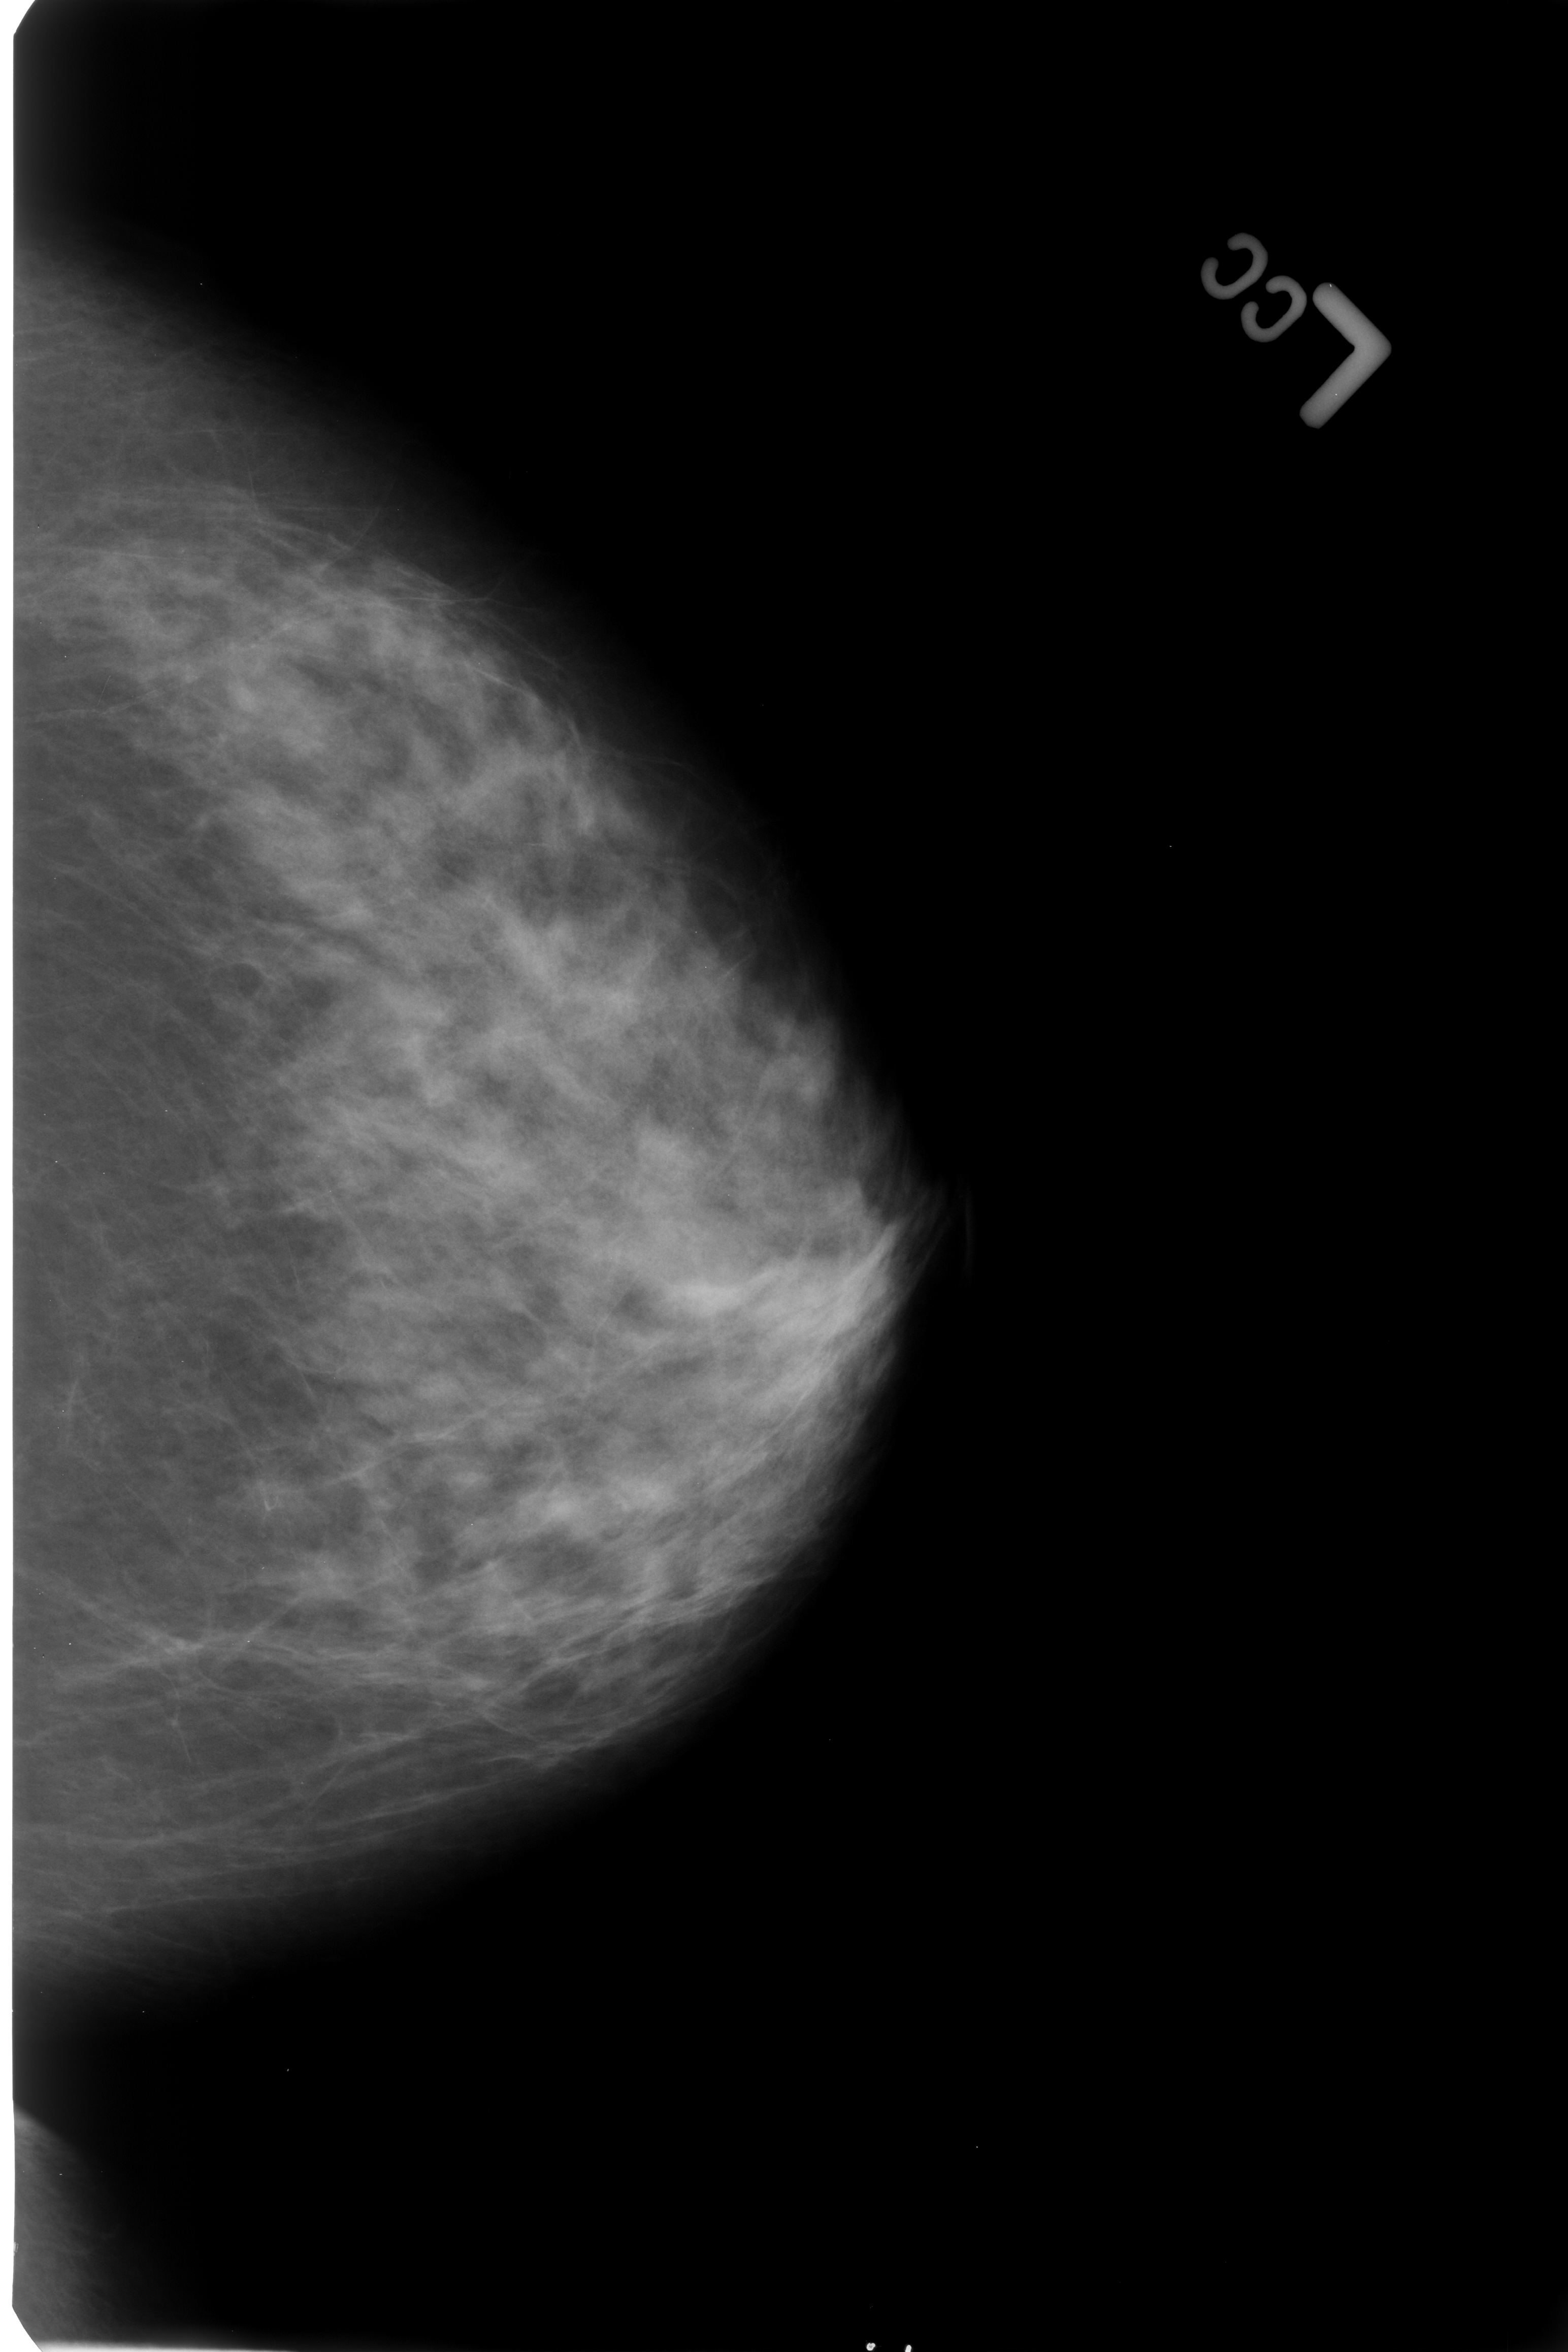
Scanned film-screen mammogram. Left breast. CC view. Breast composition: heterogeneously dense (BI-RADS density category 3 of 4). 1568 × 2352 image matrix.
Expert-marked regions of interest on this image (one box per marked abnormality):
- calcifications, morphology vascular; BI-RADS assessment category 2; subtlety rating 3 on a 1 (subtle) to 5 (obvious) scale; outcome (as recorded, no biopsy): benign without callback (not worked up further): bounding box [x1, y1, x2, y2] px = [20, 580, 428, 732]